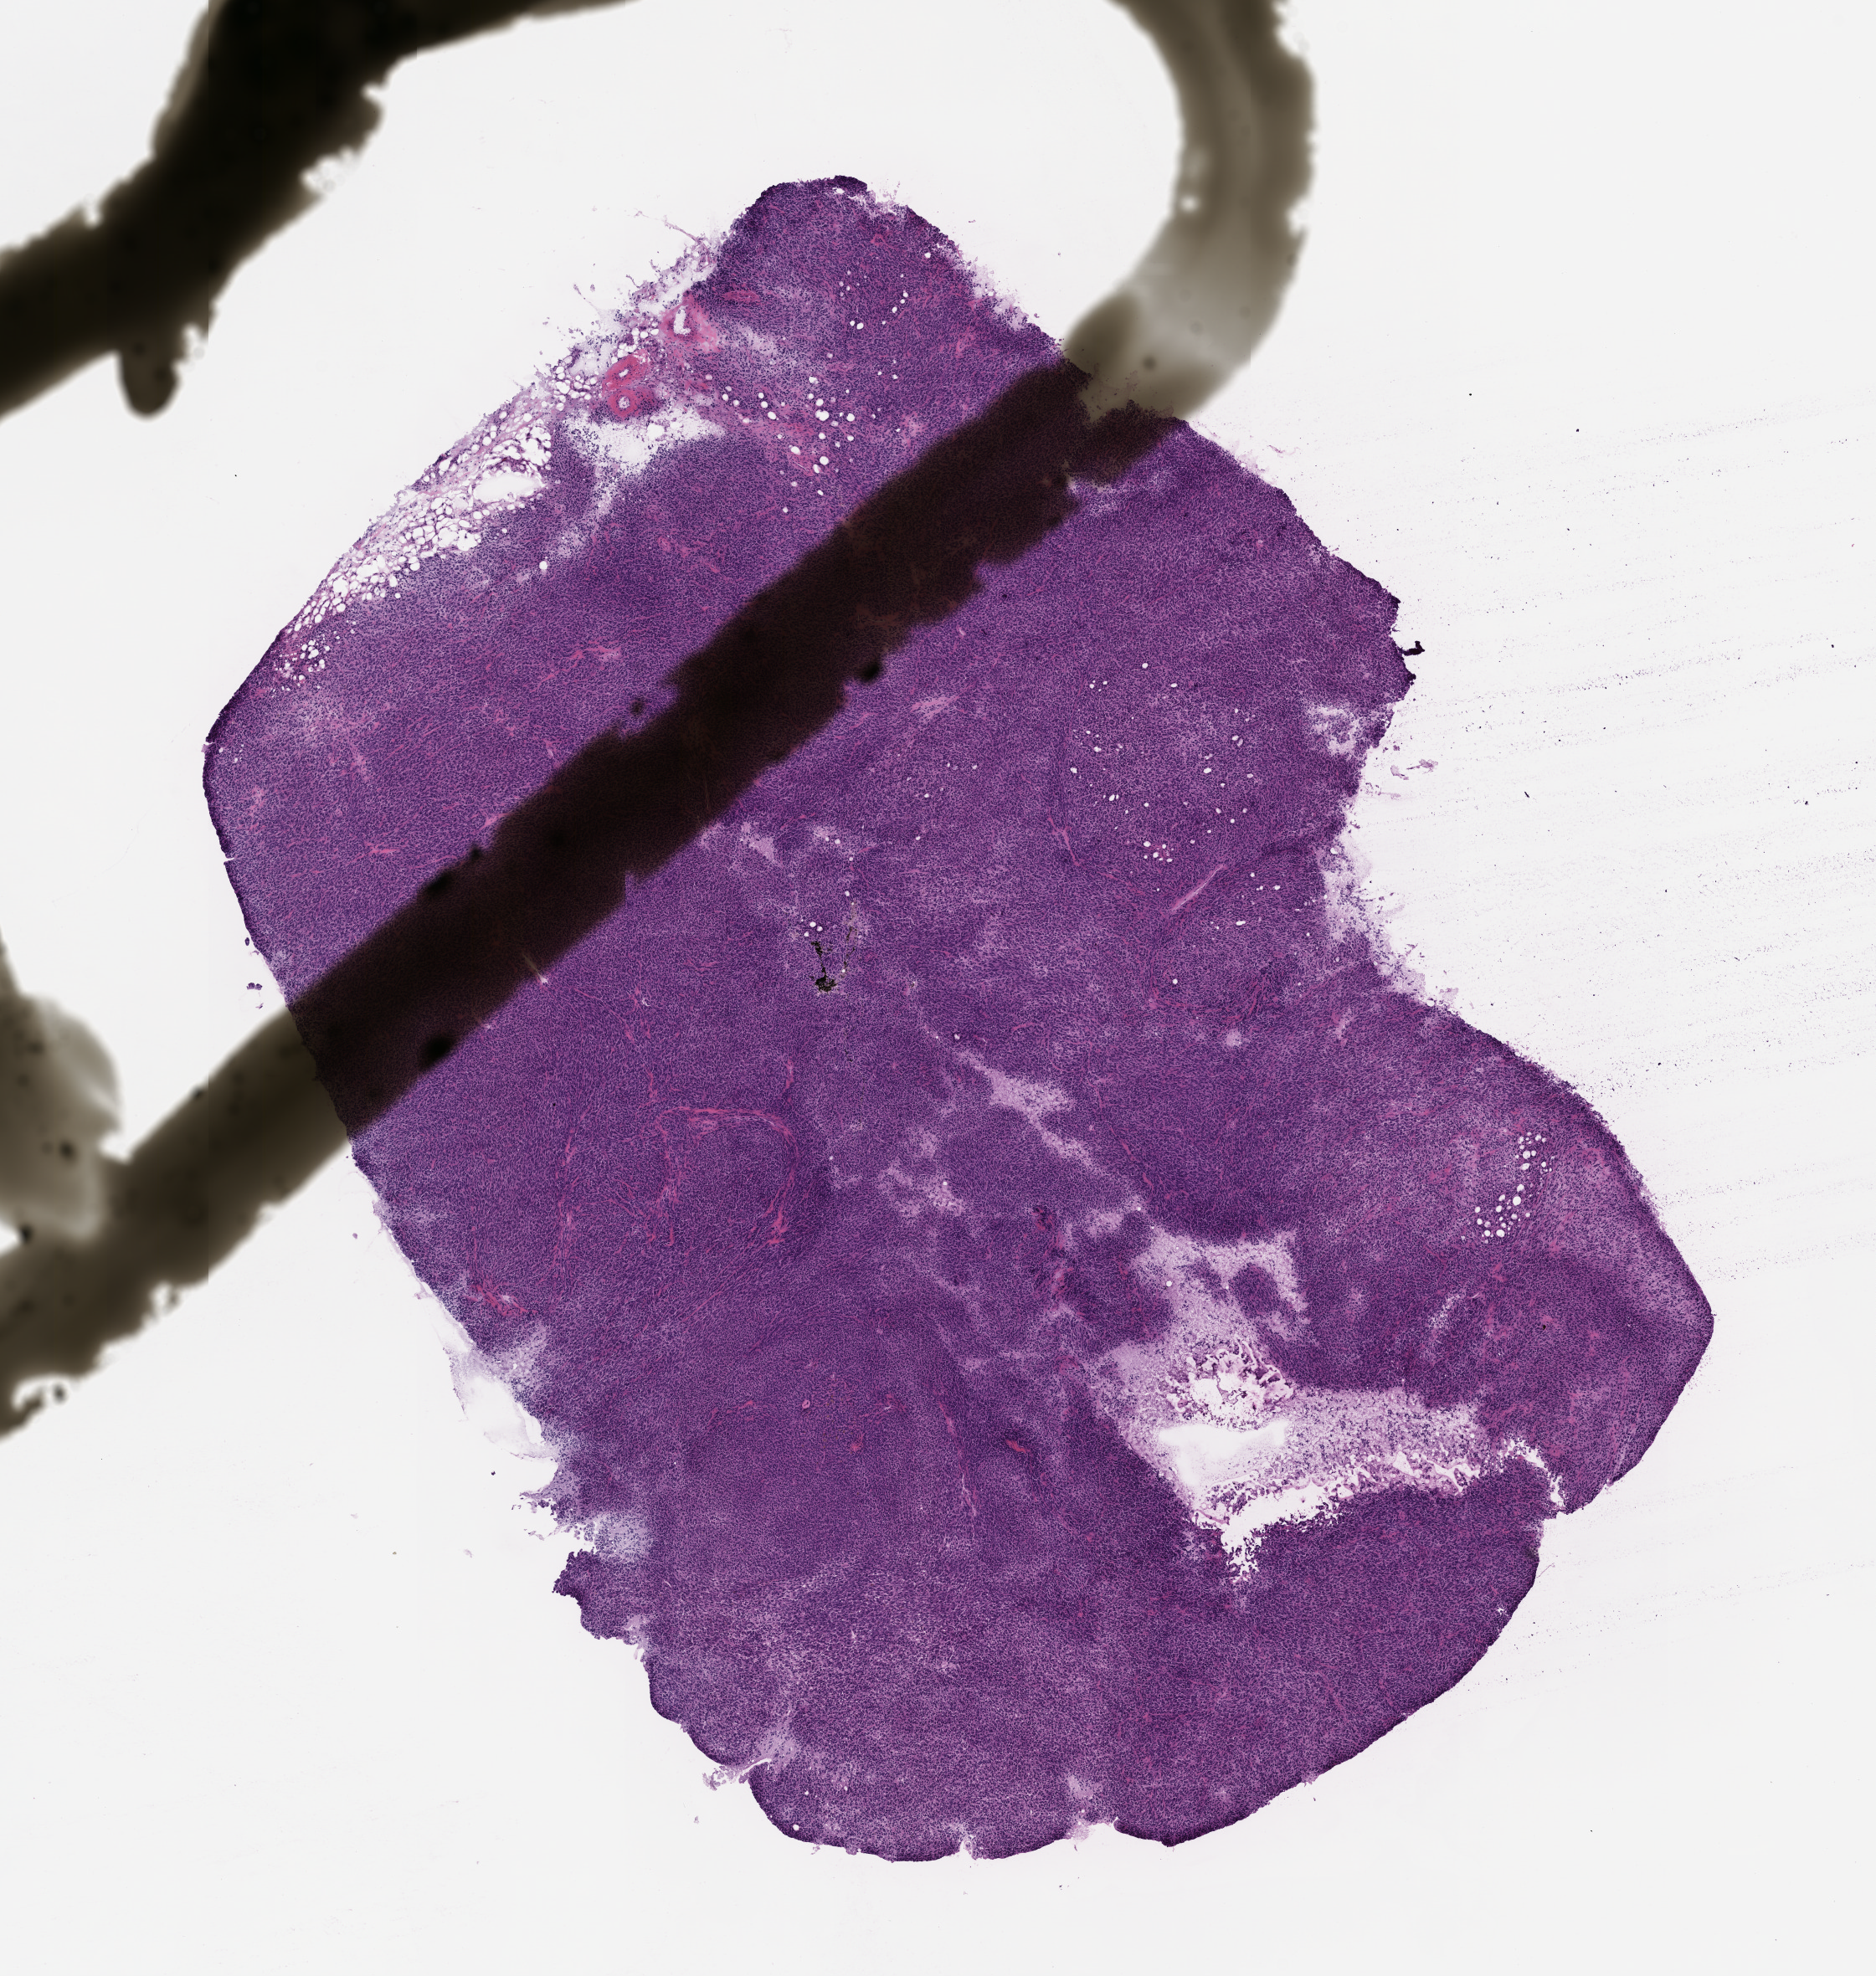
Whole-slide image, haematoxylin and eosin: patient-derived xenograft (human tumor grown in a mouse), low-resolution overview of the scanned area, about 9.0 x 9.5 mm; formalin-fixed, paraffin-embedded (FFPE) tissue; tumor site category: skin.
Originating patient diagnosis: Melanoma.